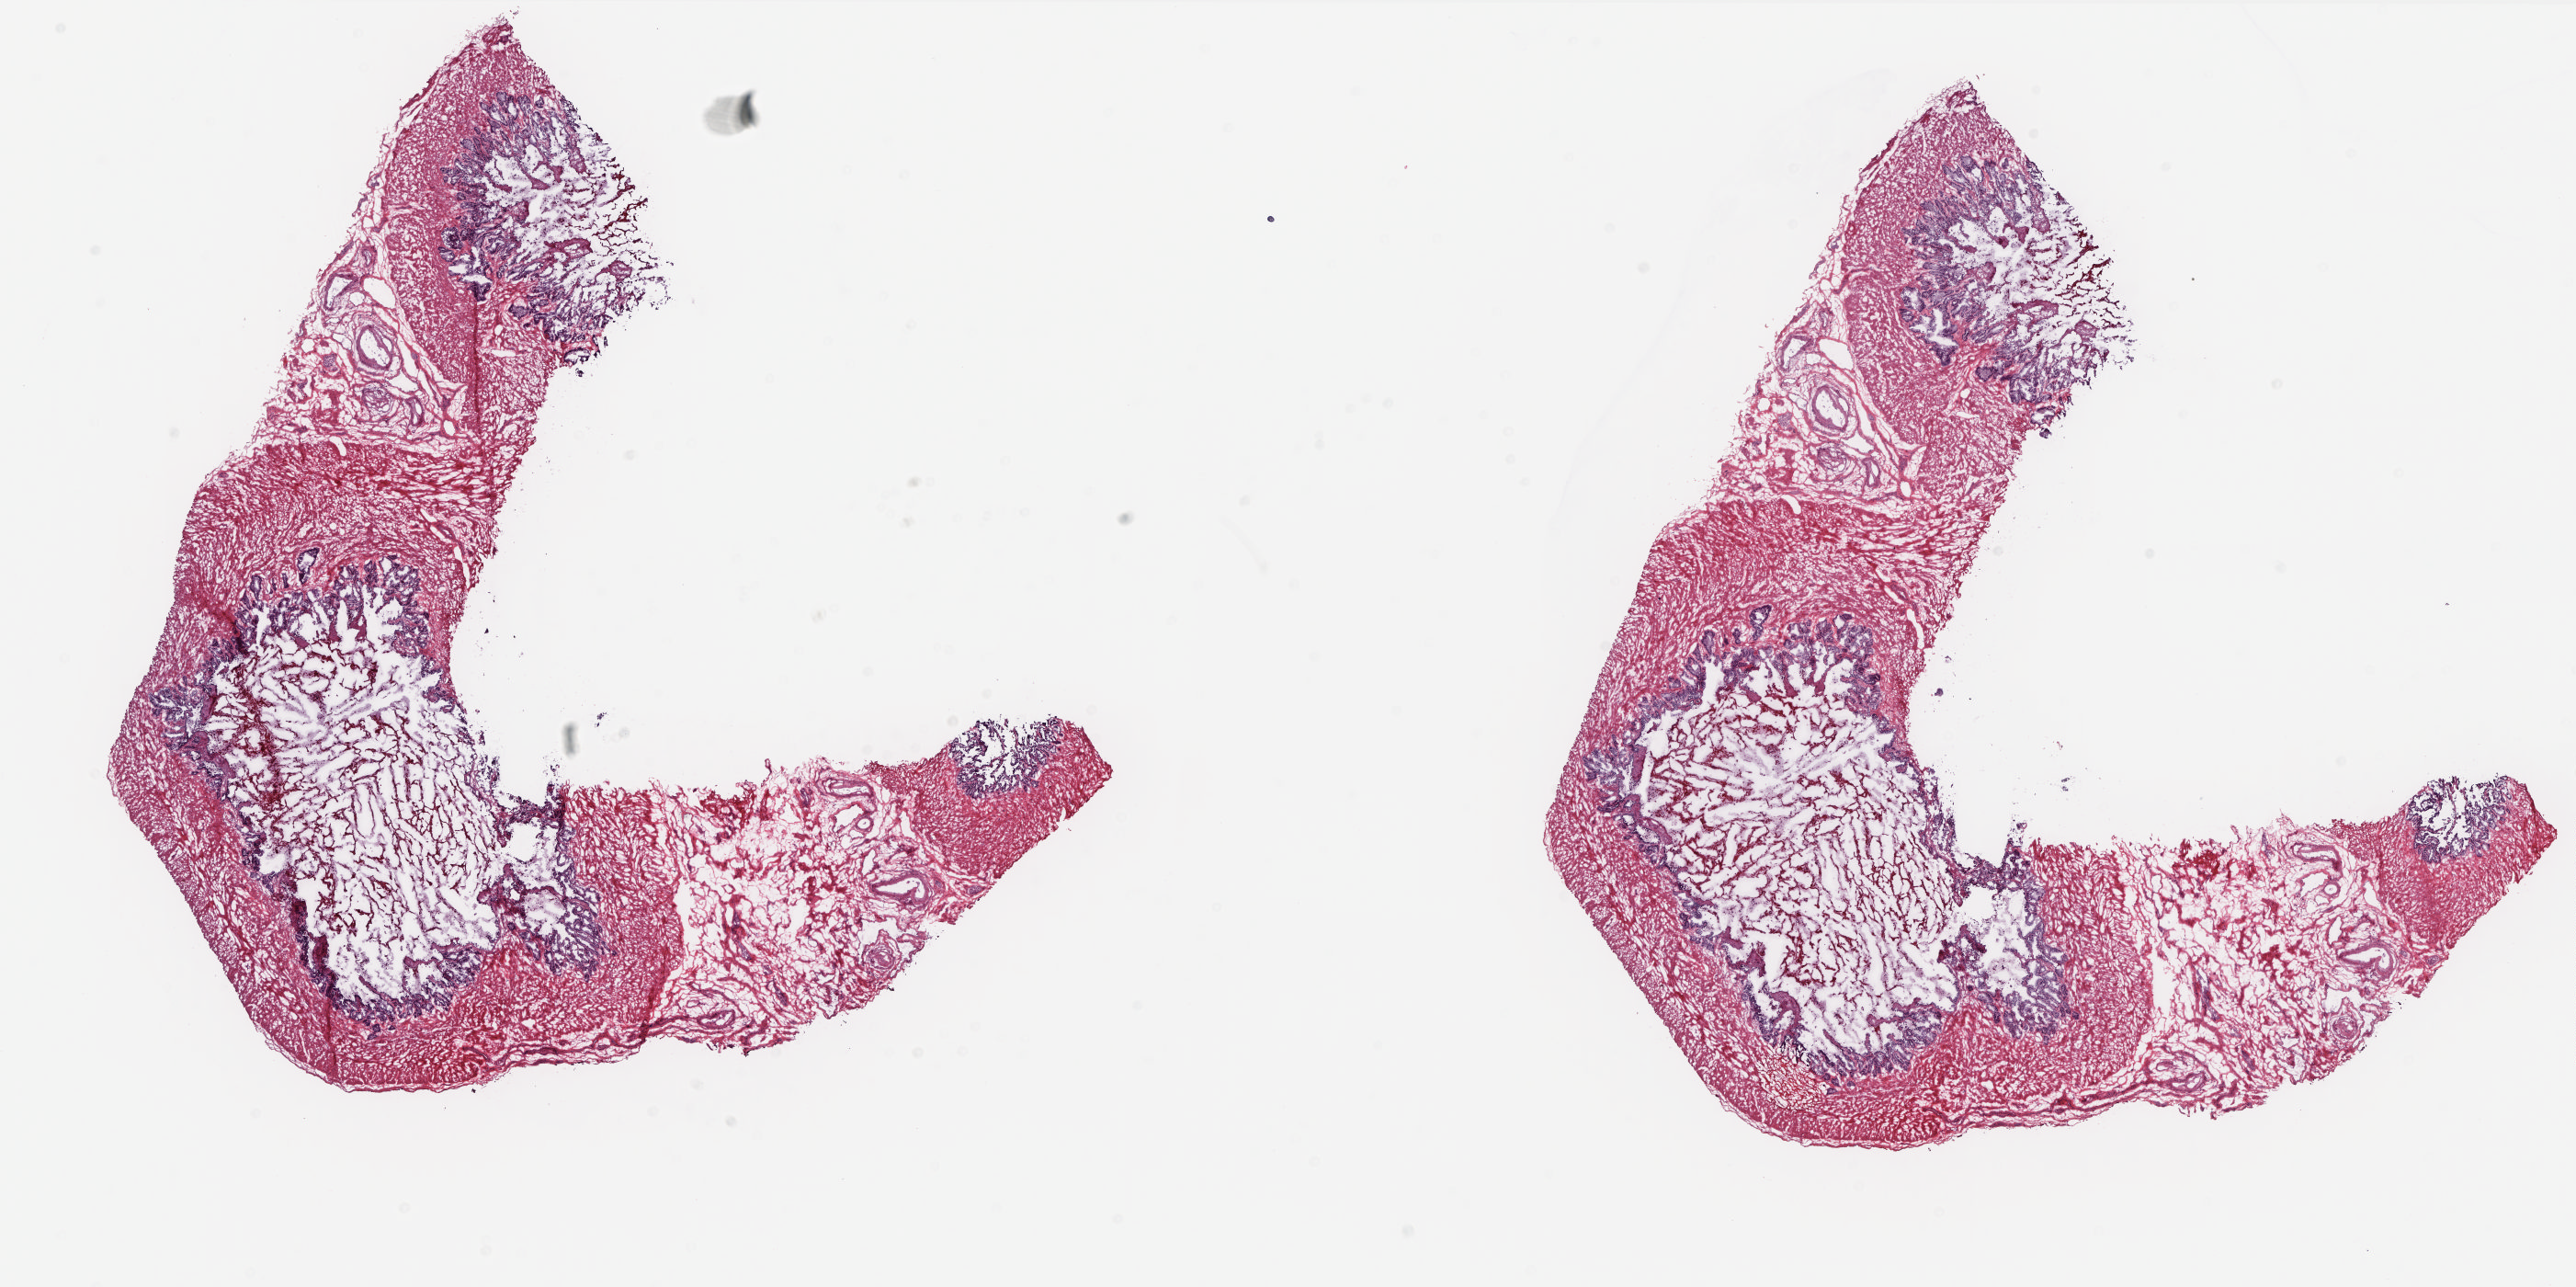
Whole-slide histology image, H&E-stained — a low-resolution overview of the entire scanned area, about 22.6 x 11.3 mm. Frozen section from the top of the tissue portion. Prostate, solid tissue normal (non-tumour tissue) sample. Patient: male, age at initial diagnosis 54 years. Pathologist review of this section (percent, as recorded): tumour cells 0%, tumour nuclei 0%, normal cells 100%, stromal cells 0%, necrosis 0%. Inflammatory infiltration, as recorded: lymphocyte infiltration 0%, monocyte infiltration 0%, neutrophil infiltration 0%.
This section: solid tissue normal (non-tumour) sample from the same patient. Patient diagnosis: Adenocarcinoma, NOS (prostate gland).